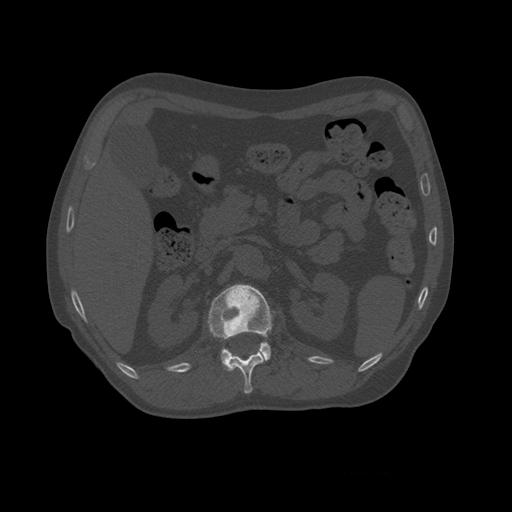
CT including the spine, one axial slice; reconstruction kernel STANDARD; 120 kVp; bone window (W 1800 / L 400 HU); 1.25 mm slice thickness; 512 × 512 image matrix, field of view 405 × 405 mm. Patient age 75 years. From the clinical record (not read from this slice): primary cancer: prostate.
Structures marked on this image (semi-automatically segmented with operator editing):
- L1 vertebra: box from (x=208, y=284) to (x=275, y=371) px
- T10 vertebra: (x=258, y=344)–(x=271, y=363)
- T11 vertebra: (x=224, y=352)–(x=264, y=394)